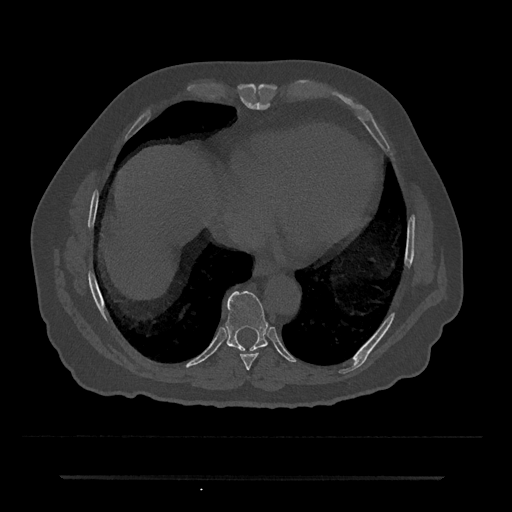
CT including the spine, one axial slice; slice 300 of 797 in the series (ordered by position); bone window (W 1800 / L 400 HU); 0.5 mm slice thickness; 512 × 512 image matrix, field of view 437 × 437 mm. Patient: male, 69 years. From the clinical record (not read from this slice): primary cancer: prostate.
Outlined on this slice (semi-automatic segmentation, software-assisted and operator-edited):
- T8 vertebra: box from (x=240, y=353) to (x=258, y=370) px
- T9 vertebra: (x=225, y=291)–(x=268, y=351)